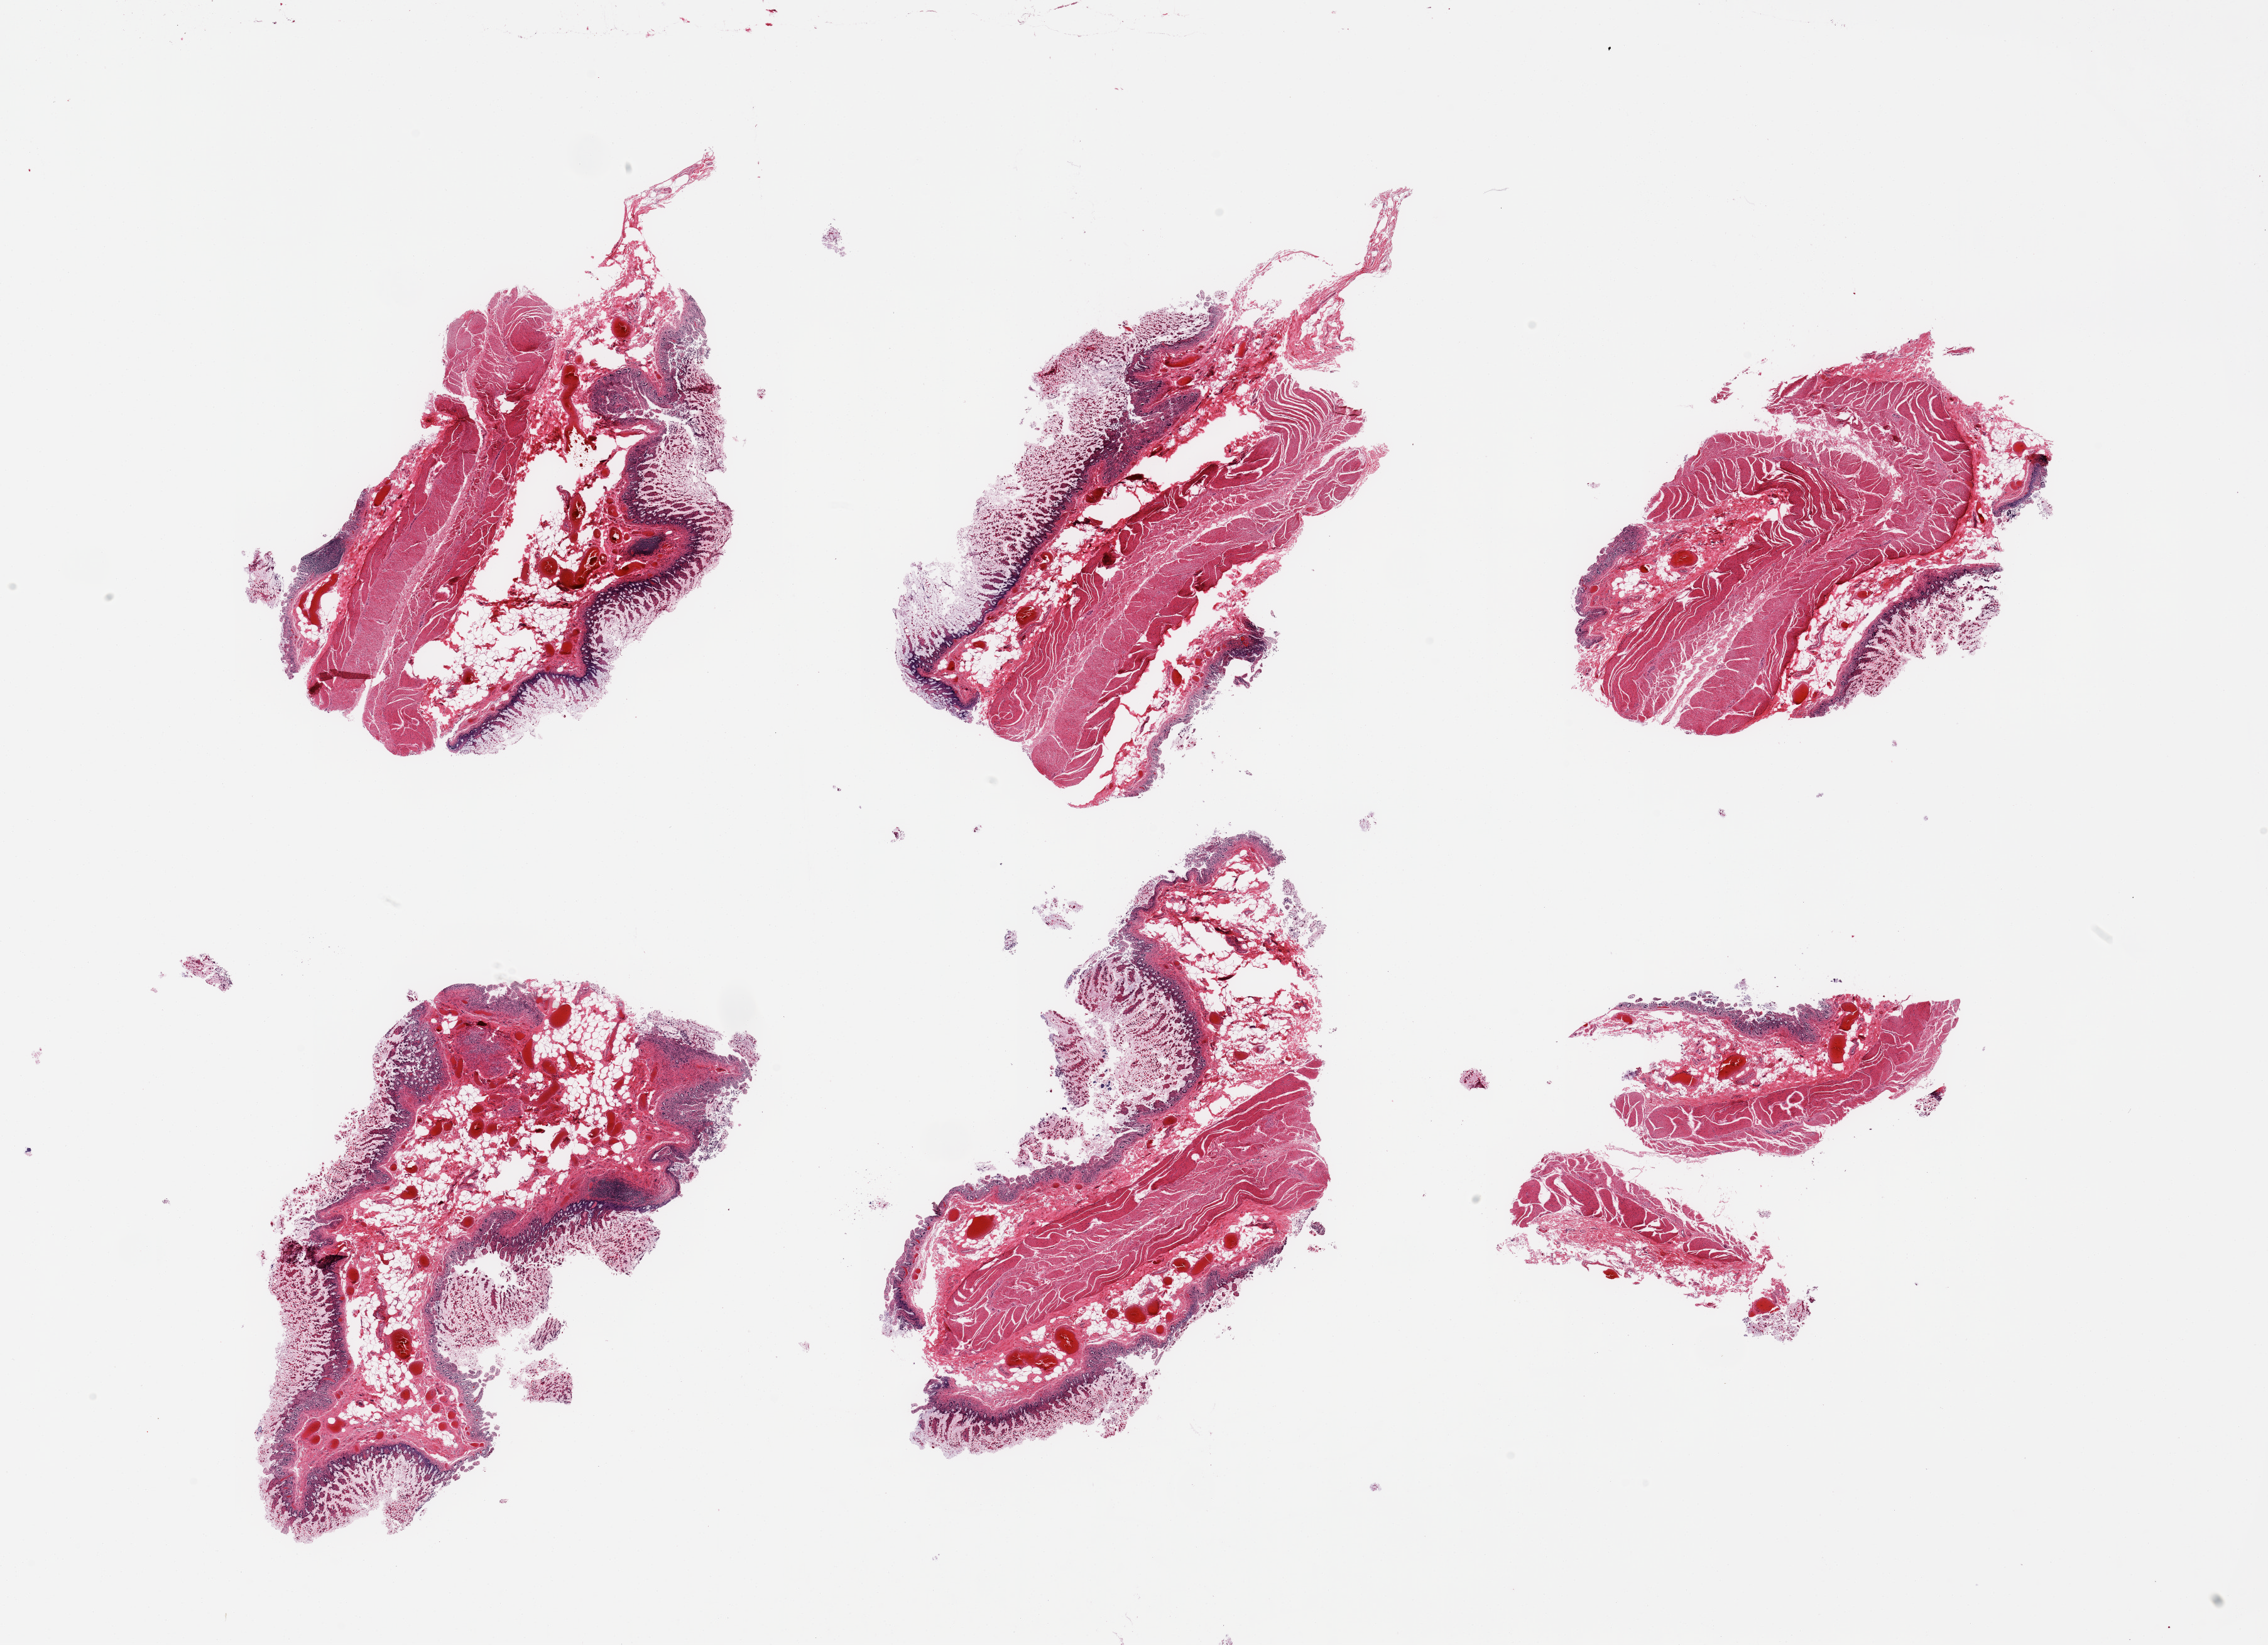
Whole-slide image, H&E stain, brightfield, low-resolution overview of the scanned area, about 28.5 x 20.7 mm. PAXgene-fixed, paraffin-embedded tissue. Sampled site (target tissue): ileum. Tissue donor sample.
* reviewer comment on this tissue sample: 6 pieces; autolyzing mucosa and muscularis (not target) with minimal lymphoid tissue